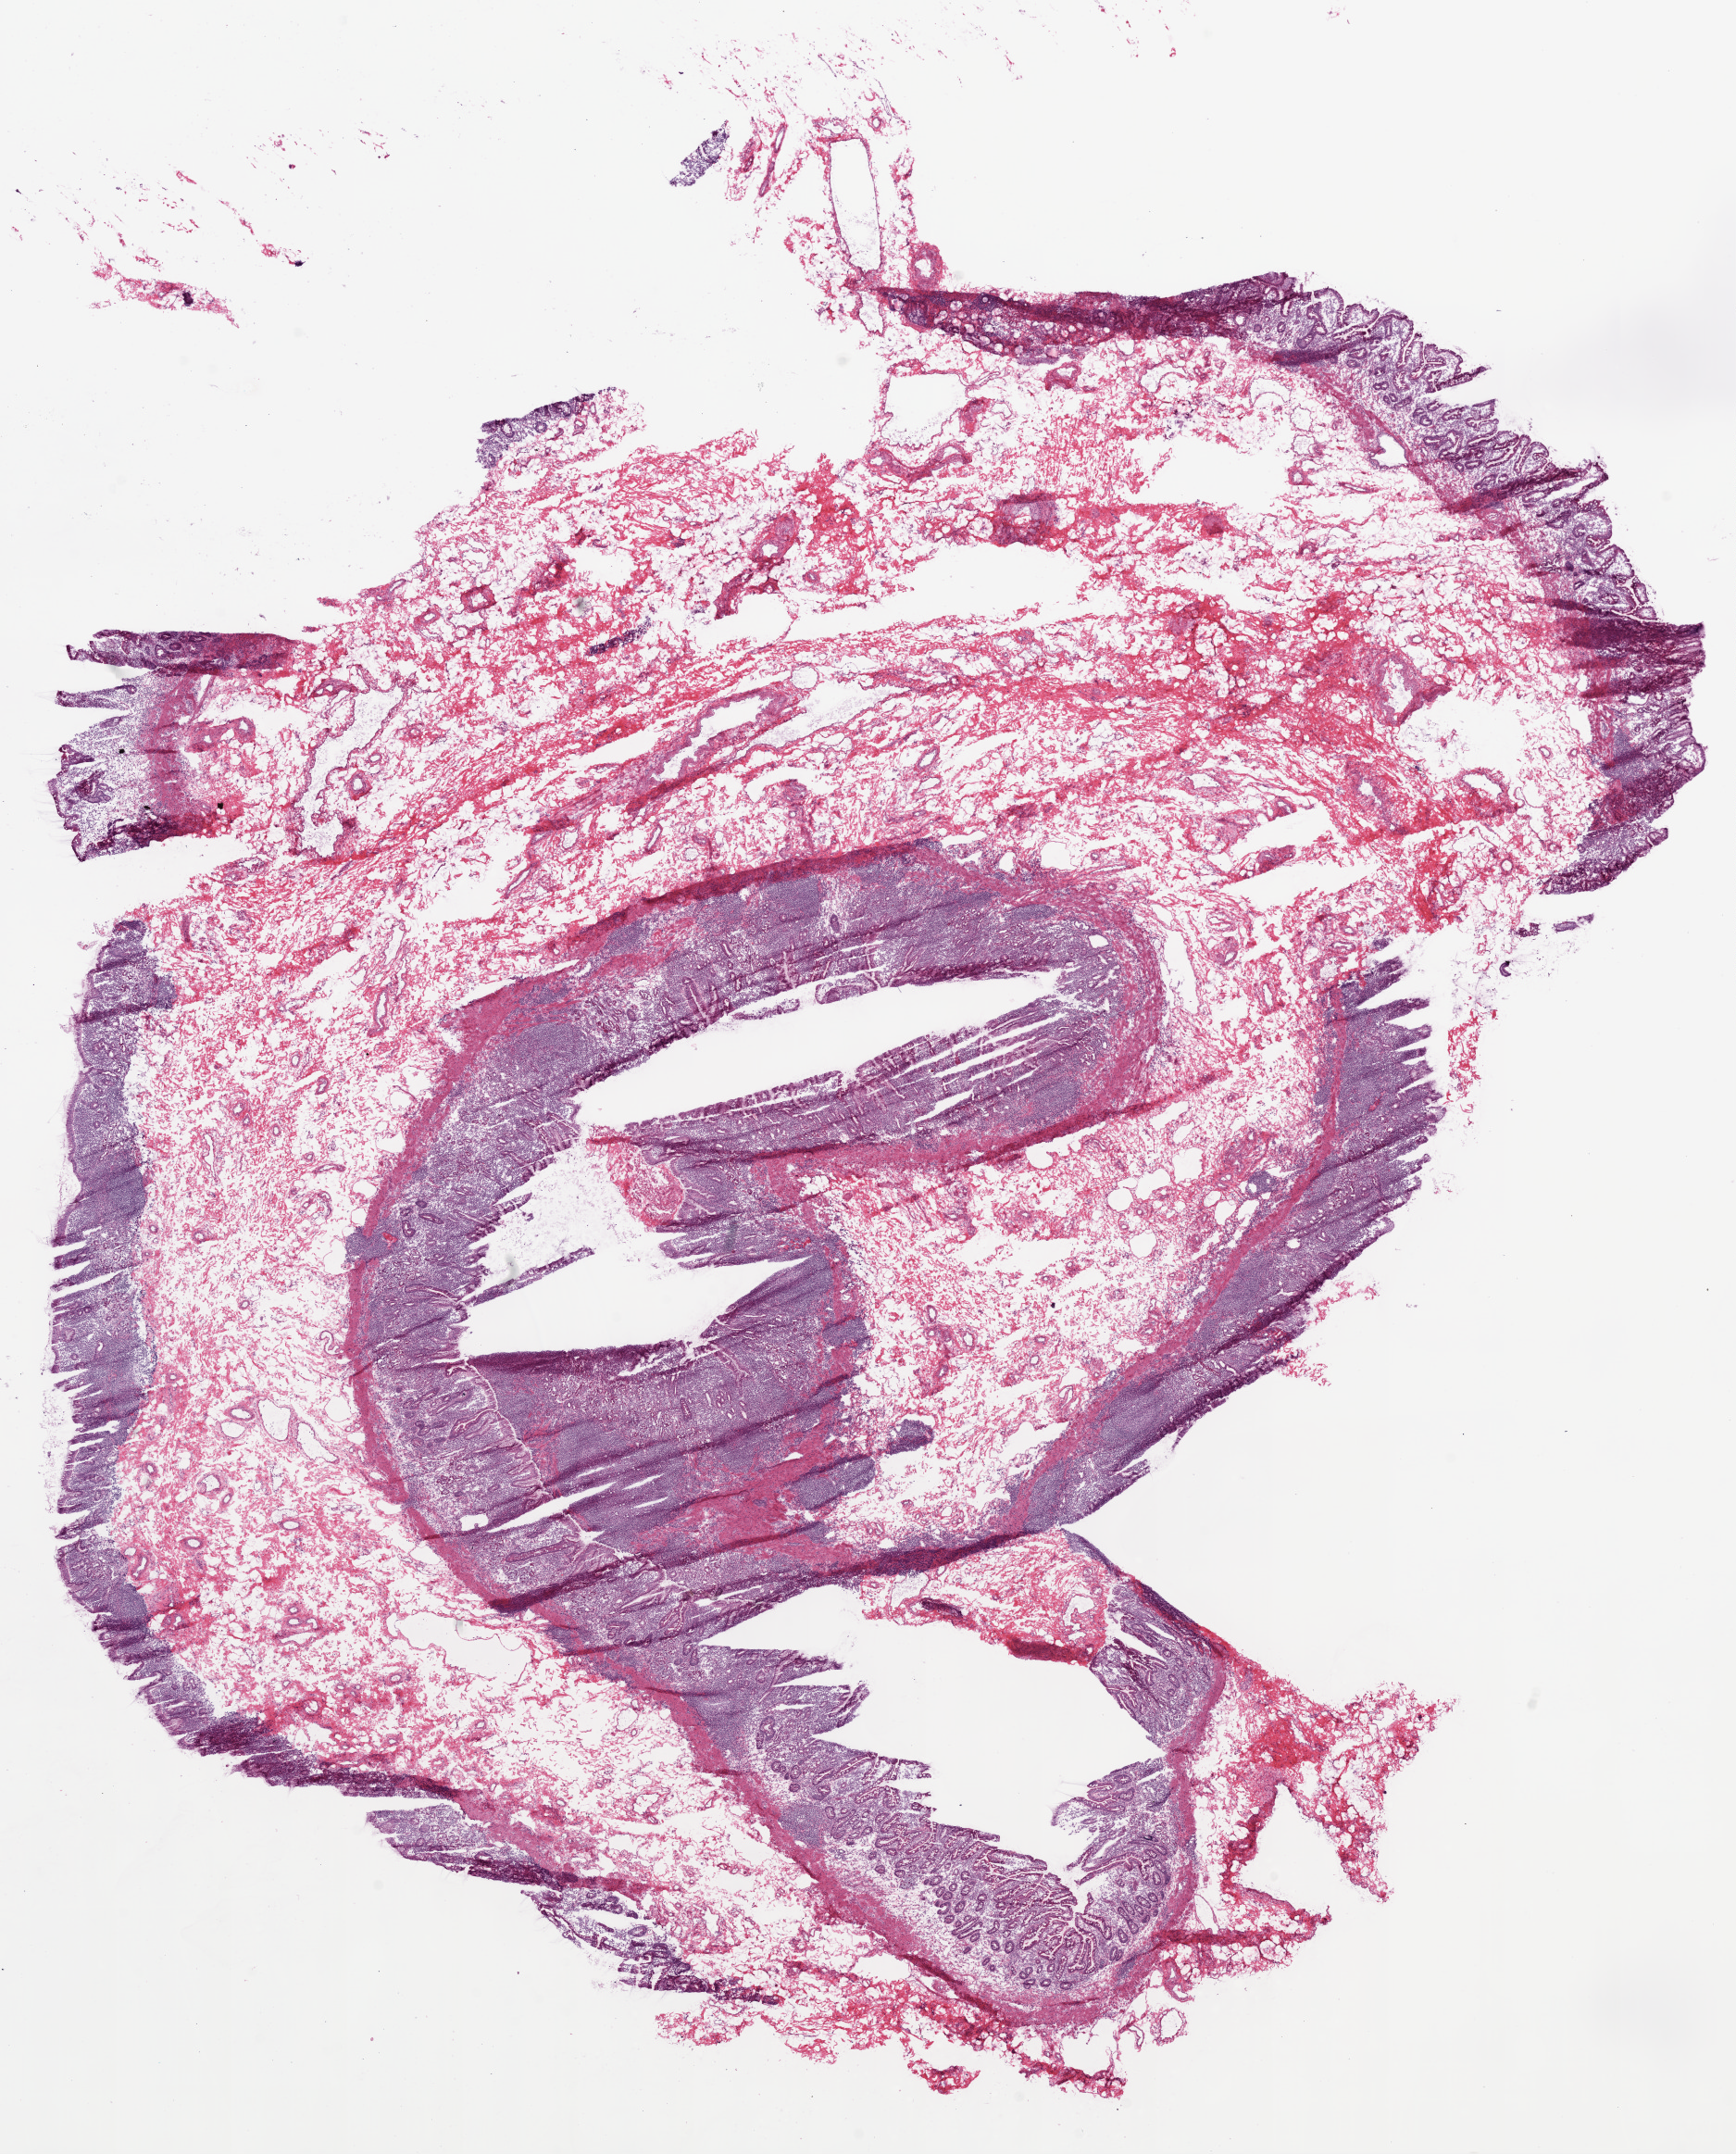
H&E whole-slide image — whole scanned area (about 15.0 x 18.7 mm, slide scanned at 20x) shown as a low-resolution overview, frozen section from the bottom of the tissue portion, sample: solid tissue normal (non-tumour tissue), stomach. Male, age 70 years at initial diagnosis.
This section: solid tissue normal (non-tumour) sample from the same patient. Patient diagnosis: Adenocarcinoma, NOS.